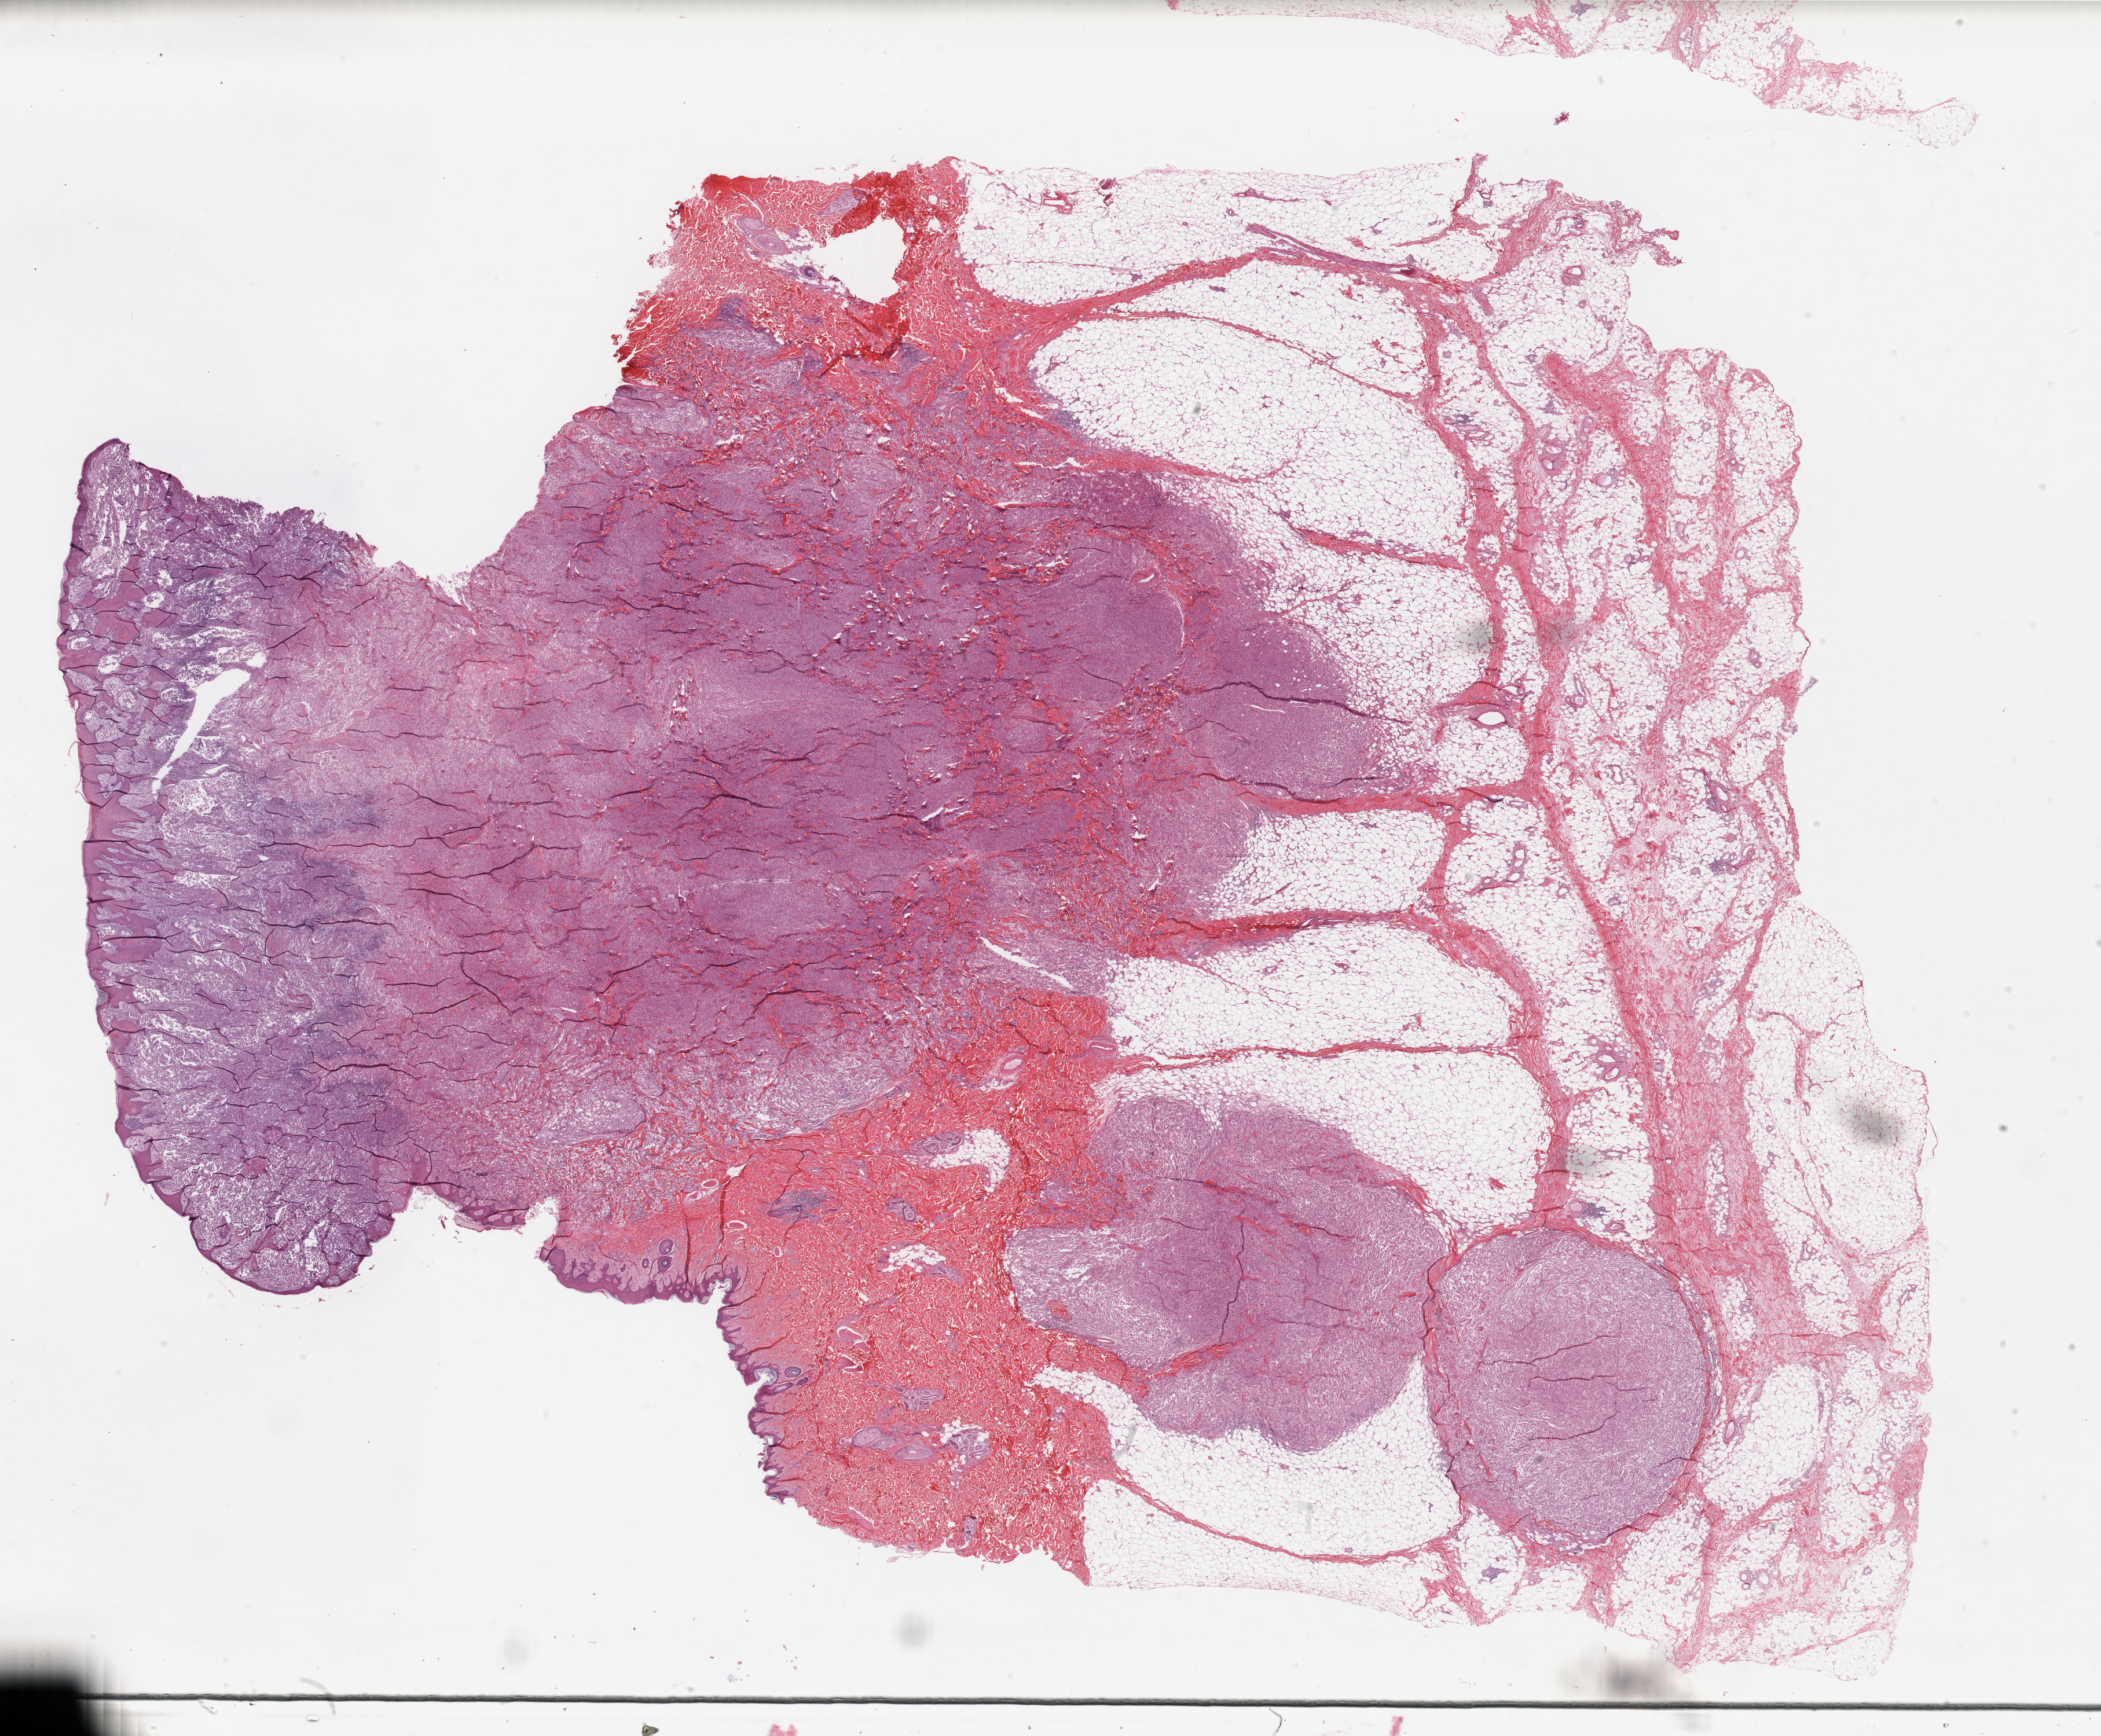
H&E-stained whole-slide image, a low-resolution overview of the entire scanned area, about 28.8 x 23.8 mm, formalin-fixed paraffin-embedded (FFPE) diagnostic section, sample: primary tumour, skin. Male patient; age at initial diagnosis 24 years.
* TNM: T4b N3 M1c
* pathologic diagnosis: Malignant melanoma, NOS
* AJCC pathologic stage: IV (6th edition)